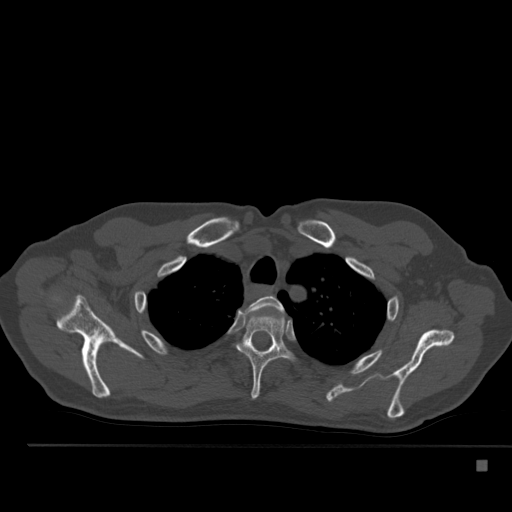
CT including the spine, one axial slice; slice 398 of 517 in the series (ordered by position); 120 kVp; bone window (W 1800 / L 400 HU); 1.5 mm slice thickness; 512 × 512 image matrix. Patient: male, 70 years. From the clinical record (not read from this slice): primary cancer: renal; vertebrae with lytic lesions (as recorded): T4, T6, T10, T12, L3, L4, L5.
Annotated regions visible in this slice (semi-automatic segmentation, software-assisted and operator-edited):
- T2 vertebra: bounding box [x1, y1, x2, y2] px = [246, 296, 285, 314]
- T3 vertebra: [237, 314, 292, 400]
- T4 vertebra: [270, 345, 272, 349]